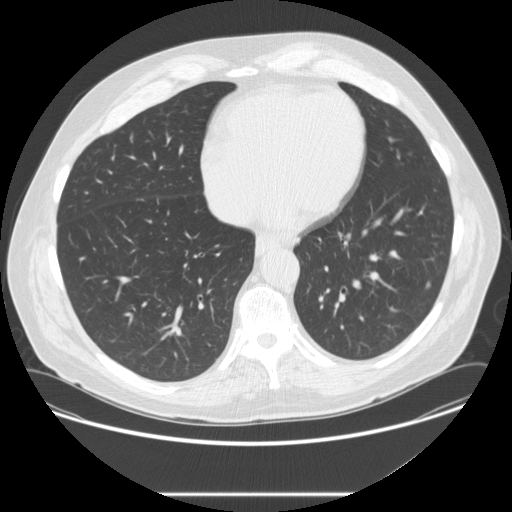
Chest CT (low-dose screening protocol), one axial image. Second screening round (one year after baseline). Lung window (W 1500 / L -600 HU). 2.5 mm slice thickness. Slice 173 of 262 in the series. Male participant, aged 67 years at enrolment. Current smoker at enrolment.
Lesion marked by an expert reader, box from (x=416, y=271) to (x=443, y=299) px. The exam's reader record, not a measurement of the box and not confirmed to be the same lesion: non-calcified nodule or mass ≥4 mm, left lower lobe, 4 × 4 mm, poorly defined margins, soft tissue attenuation, pre-existing on the prior screen: yes; interval growth: no. Official screen result: positive, other. Participant outcome: lung cancer diagnosed 72 days after this screen — adenocarcinoma, NOS, left lower lobe, moderately differentiated (G2), stage IIA (AJCC 6th edition), 6 mm at pathology.